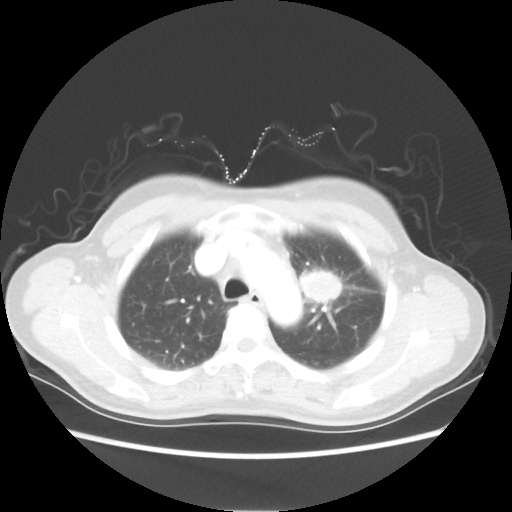
Chest CT, one axial slice. Reconstruction kernel STANDARD. Lung window (W 1500 / L -600 HU). 5 mm slice thickness. 512 × 512 image matrix, field of view 360 × 360 mm. Female patient, age 53 years. Case-level facts recorded for this patient, not image findings: clinical TNM (as recorded): T1c N0 M0.
Annotated regions visible in this slice (rectangle marked by the reading radiologist):
- lung tumour (recorded histology: adenocarcinoma): bounding box [x1, y1, x2, y2] px = [293, 264, 342, 313]
- lung tumour (recorded histology: adenocarcinoma): [294, 262, 346, 311]